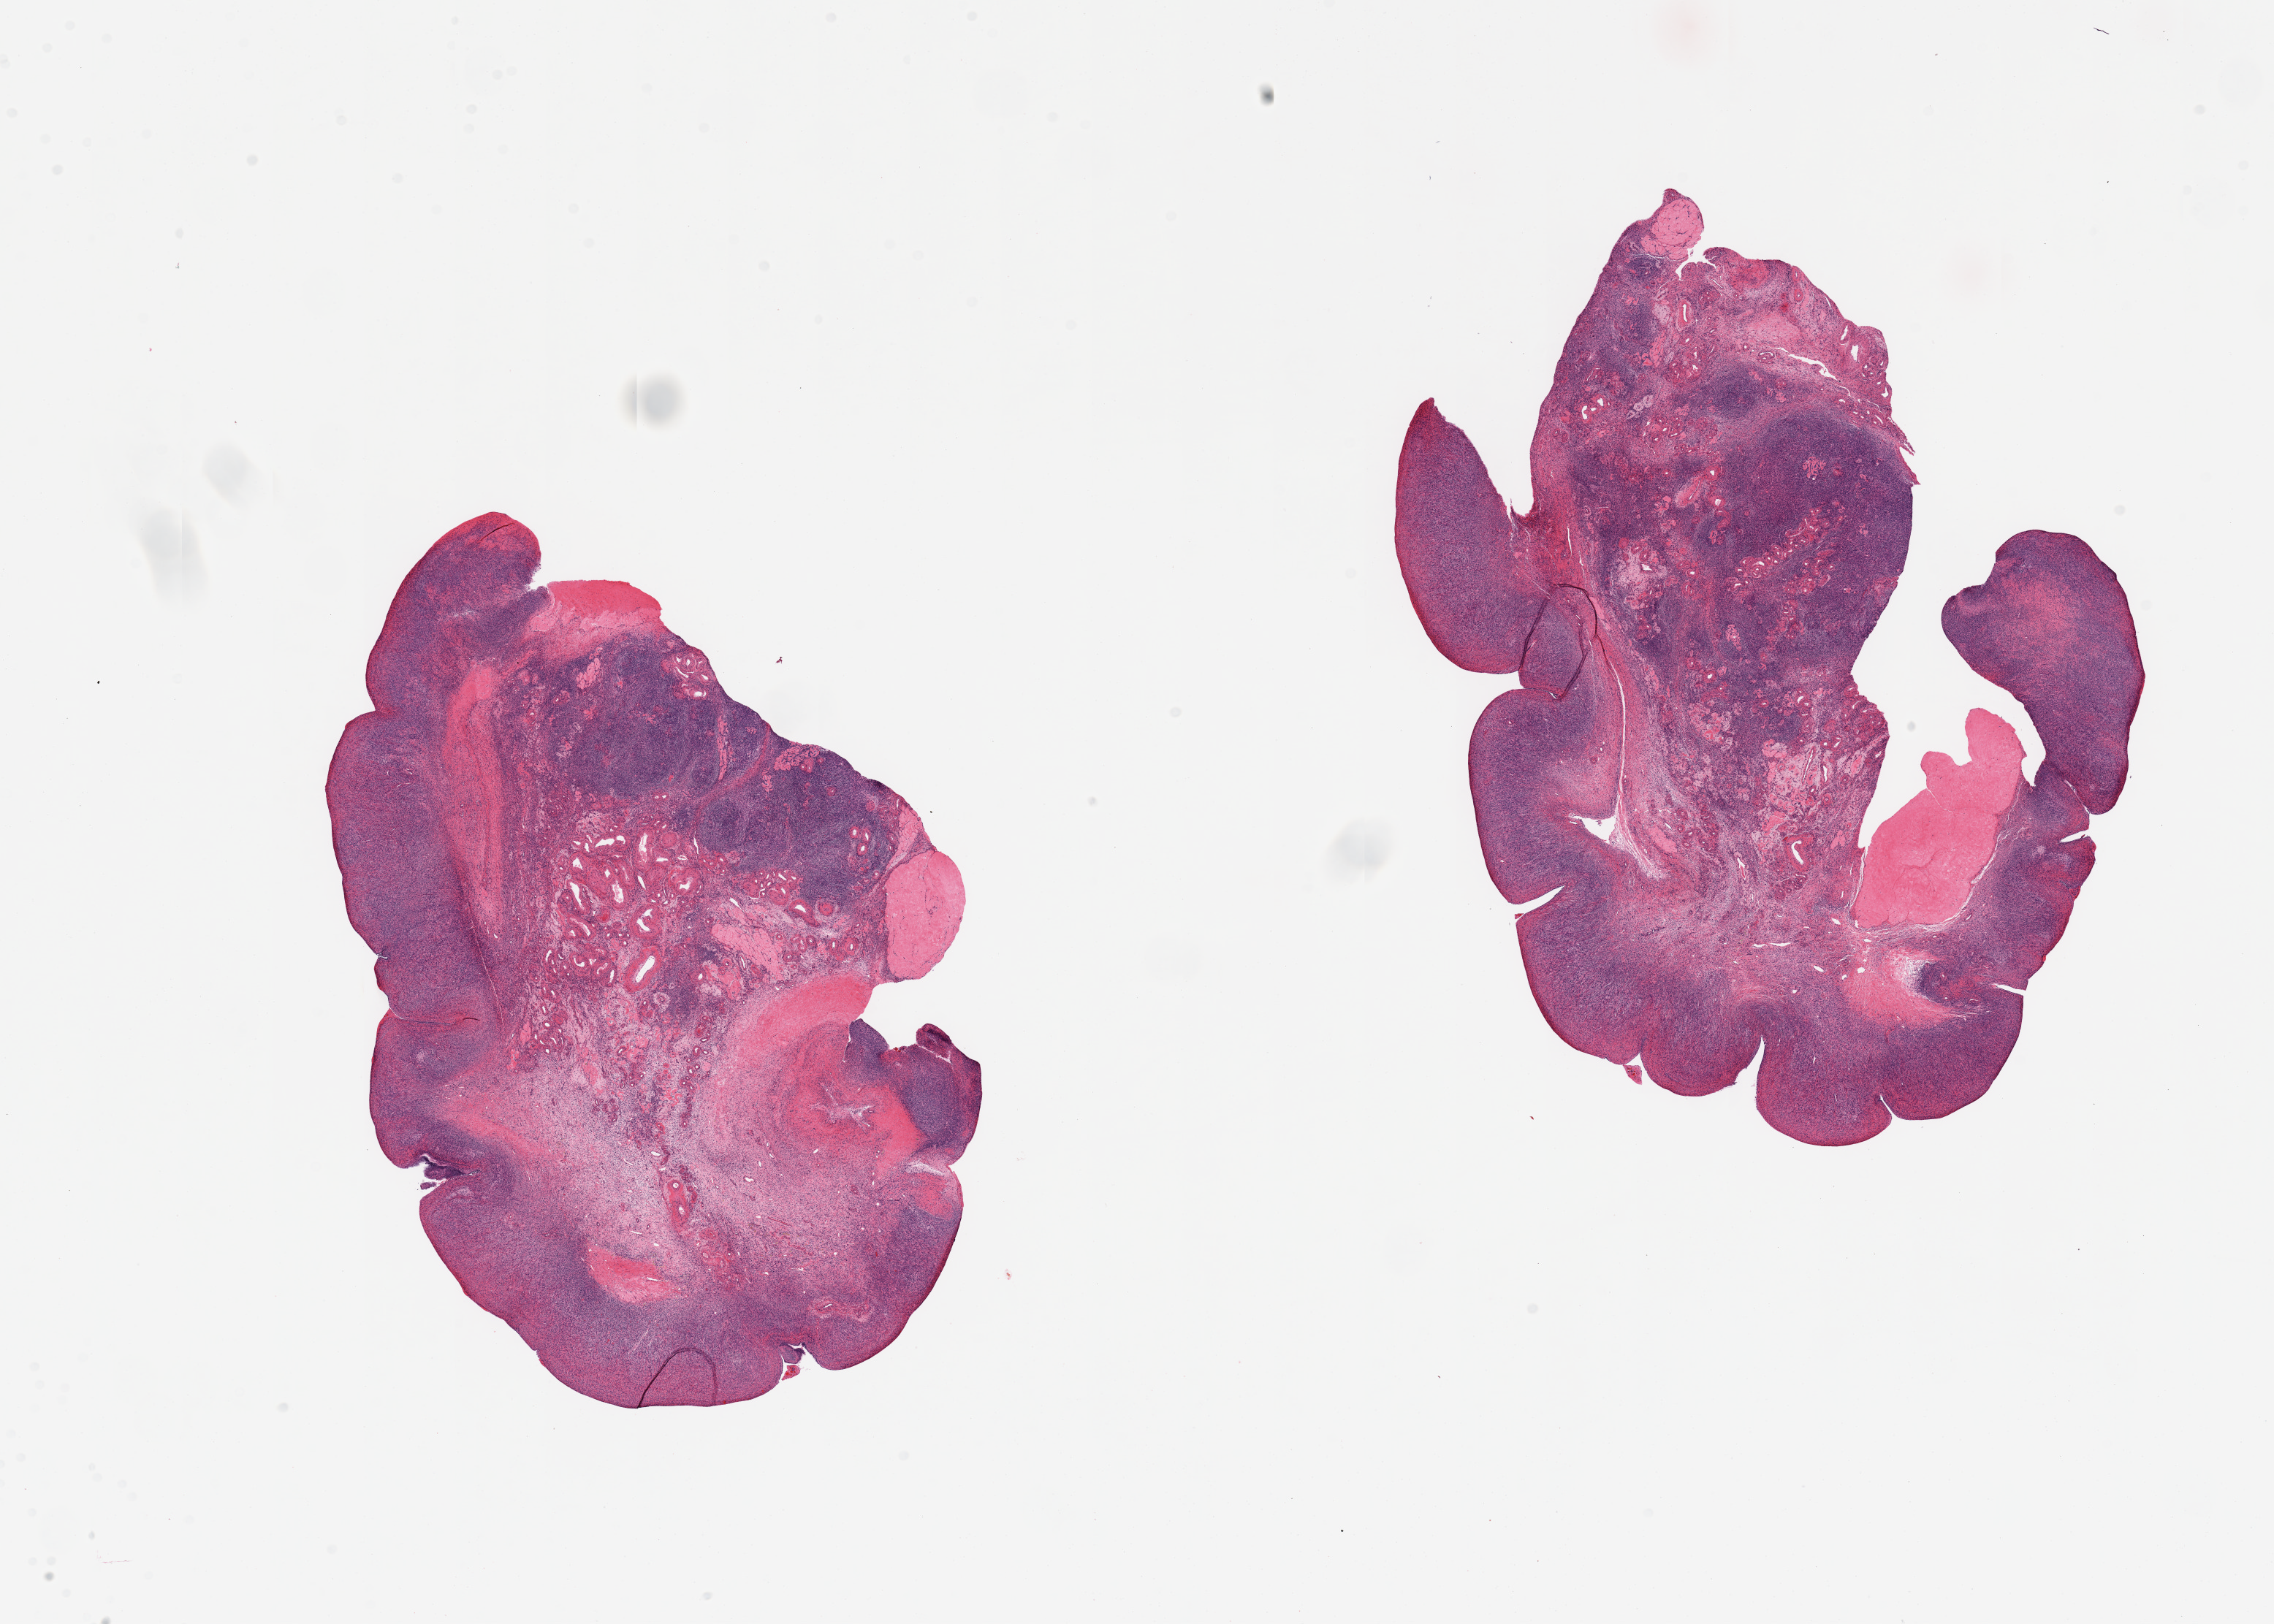
Digitized hematoxylin and eosin (H&E)-stained section, whole scanned area (about 24.6 x 17.6 mm, from a 20x scan) shown as a low-resolution overview. PAXgene-fixed, paraffin-embedded tissue. Target tissue: ovary. Donor tissue sample. Donor: female.
* pathologist's review note for this sample: 2 pieces; corpora albicans; inactive